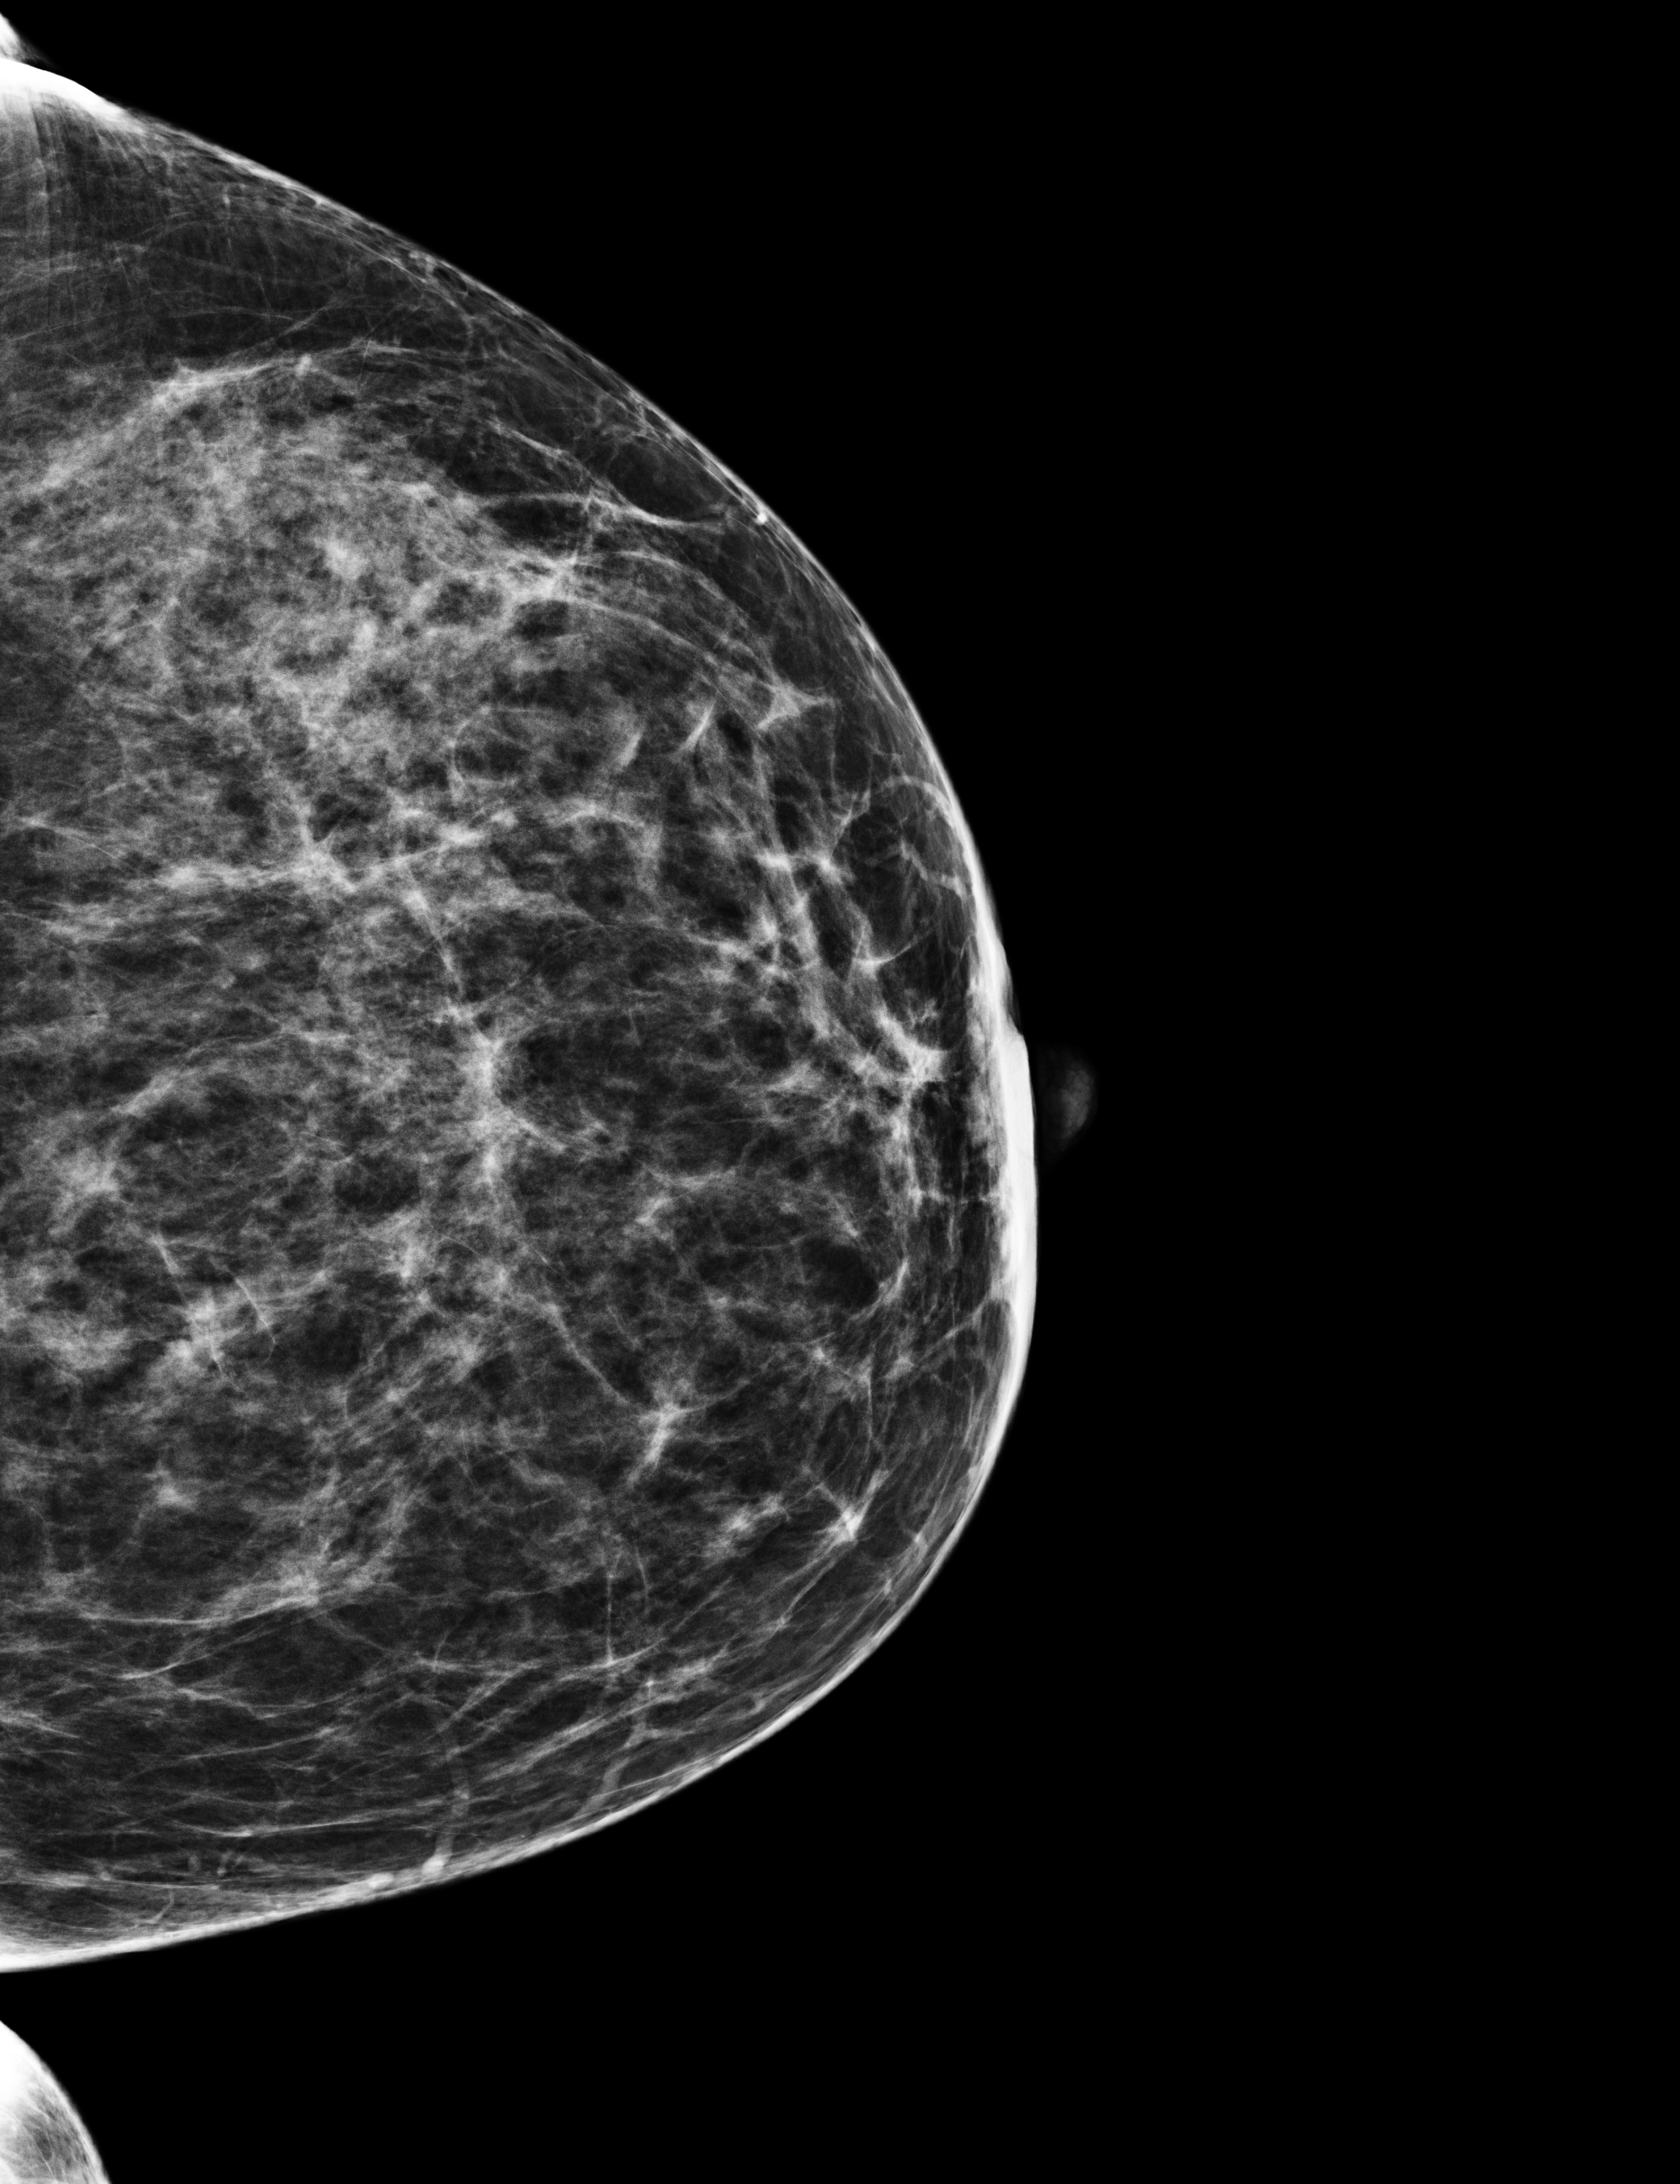
Full-field digital mammogram (FFDM), left breast, craniocaudal (CC) view, screening examination, system: Selenia Dimensions. Patient: female, 62 years.
Breast density at the screening exam (both breasts): heterogeneously dense (BI-RADS density category c). Final BI-RADS assessment for this screening round (tomosynthesis exam, both breasts): category 1. Recall: no recall after this screen.